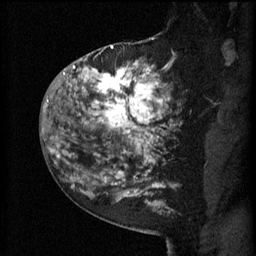
Breast MRI (dynamic contrast-enhanced), one sagittal slice; slice 39 of 60 in the series (ordered by position); 3 images stored at this slice position (order not interpretable as contrast timing); 1.5 T; TE 4.2 ms, TR 11 ms; 2 mm slice thickness; 256 × 256 image matrix, field of view 180 × 180 mm. Patient: female, 52 years.
Outlined on this slice (semi-automatic segmentation, software-assisted and operator-edited):
- analysis volume of interest (the breast-tissue region the enhancement analysis was run in; not a lesion): bounding box <81,52,174,157> (left, top, right, bottom; pixels)
- tumour enhancement mask (voxels above the 70 % enhancement threshold inside the analysis volume of interest): <83,54,171,157>